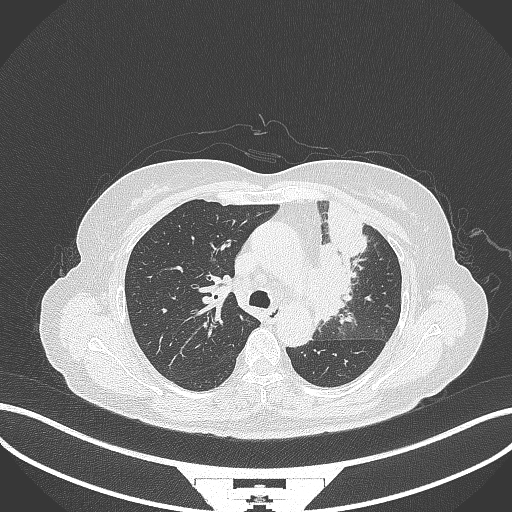
Chest CT, one axial slice; slice 227 of 382 in the series (ordered by position); reconstruction kernel B70f; 120 kVp; lung window (W 1500 / L -600 HU); 1 mm slice thickness; 512 × 512 image matrix, field of view 400 × 400 mm. Patient: female, 64 years. Case-level facts recorded for this patient, not image findings: clinical TNM (as recorded): T2a N2 M0.
Outlined on this slice (bounding box drawn by a radiologist):
- lung tumour (recorded histology: adenocarcinoma): bounding box [x1, y1, x2, y2] px = [308, 198, 368, 326]